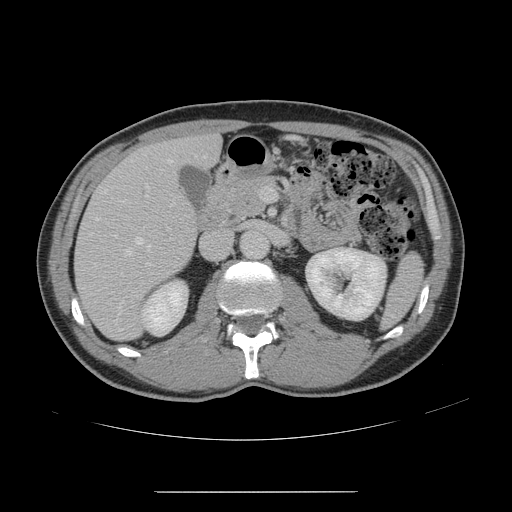
Contrast-enhanced abdominal CT, one axial slice. Slice 74 of 178 in the series (ordered by position). 120 kVp. Intravenous contrast given. Soft-tissue window (W 400 / L 40 HU). 512 × 512 image matrix. Male patient, age 53 years. From the clinical record (not read from this slice): diagnosis: colorectal cancer liver metastases, imaged before liver resection; multiple liver metastases: yes; largest metastasis: 2.4 cm; disease in both lobes: no.
Annotated regions visible in this slice (expert manual segmentation):
- hepatic veins: bounding box (x1, y1, x2, y2) in pixels: (94, 160, 172, 309)
- liver: (75, 136, 221, 340)
- planned liver remnant (the part of the liver to remain after resection): (181, 137, 220, 164)
- portal vein (with intrahepatic branches): (146, 187, 267, 202)